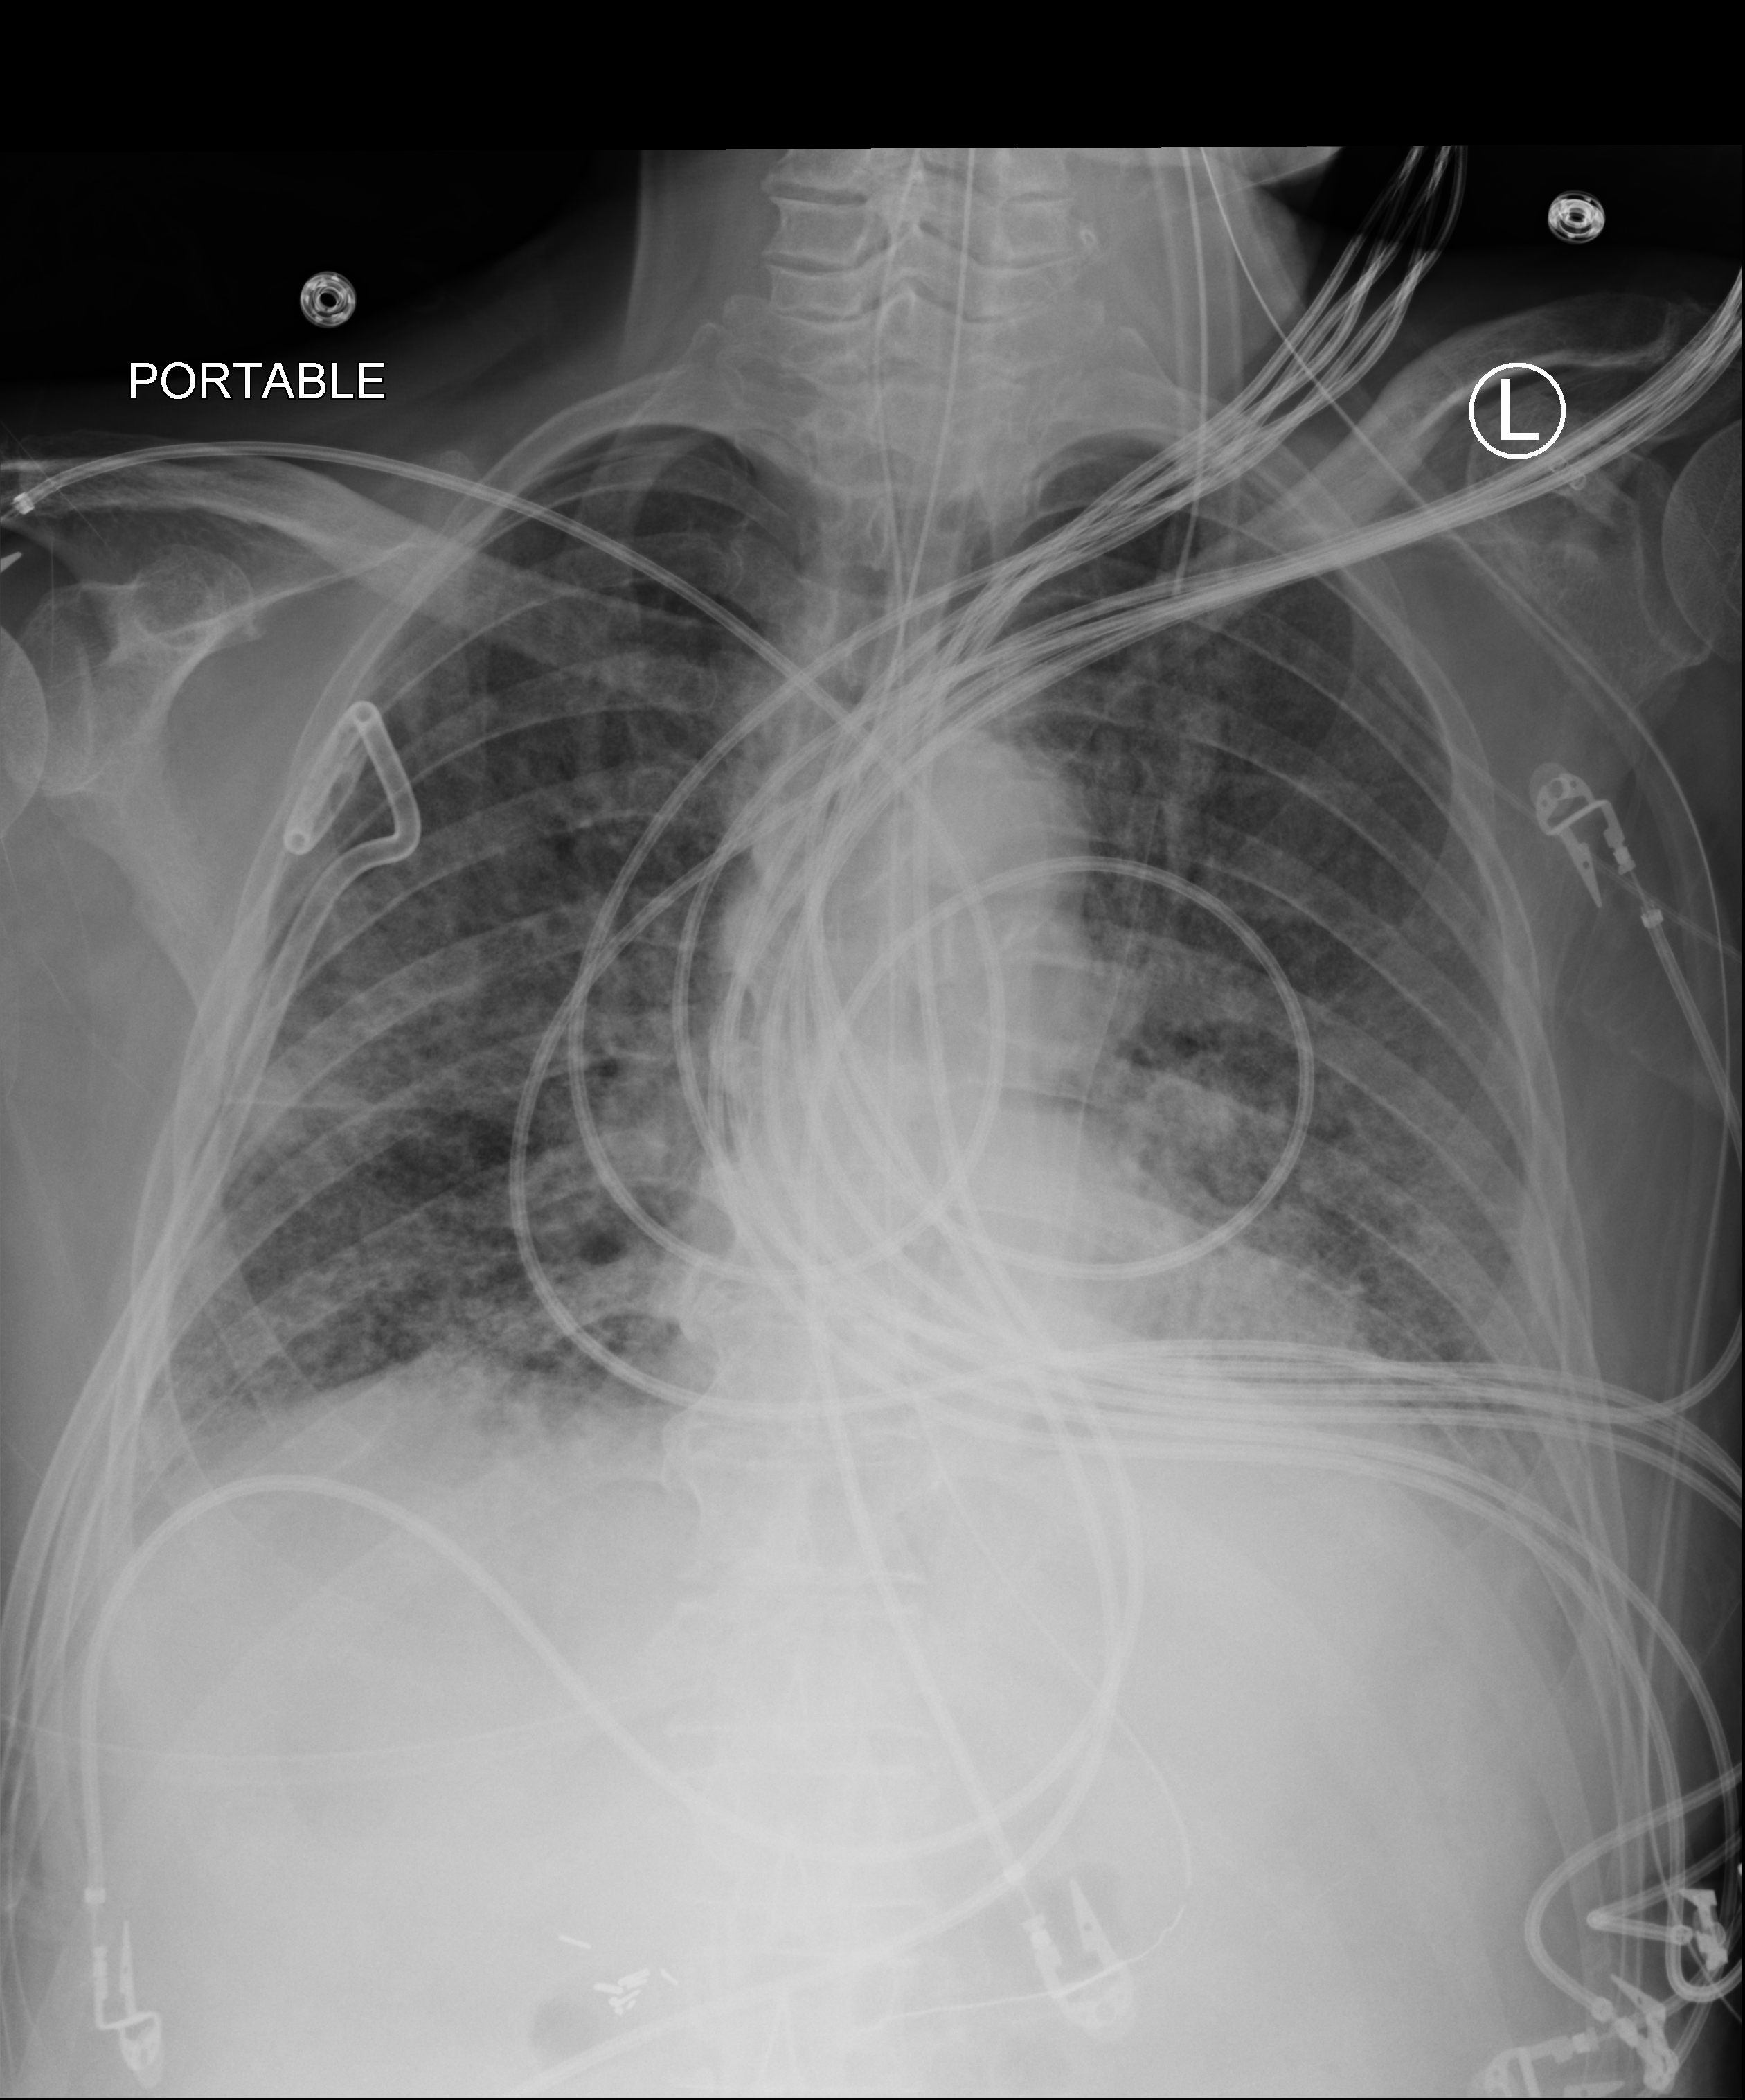
Portable chest radiograph, anteroposterior (AP) projection. Male patient hospitalised with COVID-19, age 75–90 years.
Admission-level facts for this patient (not findings on this image; timing relative to this image not recorded):
- COPD (admission record): no
- chronic kidney disease (admission record): no